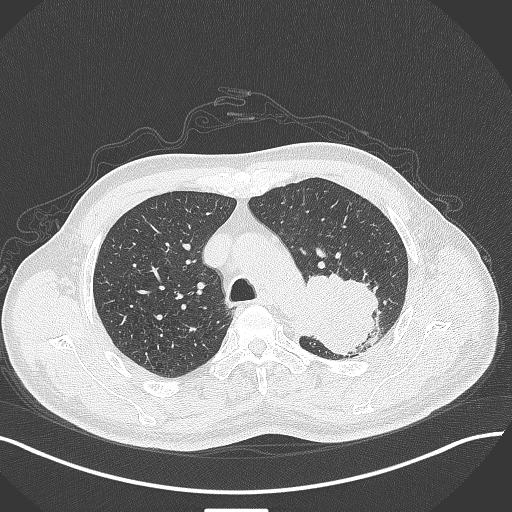
Chest CT, one axial slice; position 314 of 429 along the scan axis; reconstruction kernel B70f; lung window (W 1500 / L -600 HU); 1 mm slice thickness; 512 × 512 image matrix, field of view 400 × 400 mm. Male patient, age 55 years. From the clinical record (not read from this slice): clinical TNM (as recorded): T3 N0 M1c; histopathological grade: G3.
Annotated regions visible in this slice (rectangle marked by the reading radiologist):
- lung tumour (recorded histology: adenocarcinoma): bounding box (x1, y1, x2, y2) in pixels: (297, 275, 387, 353)